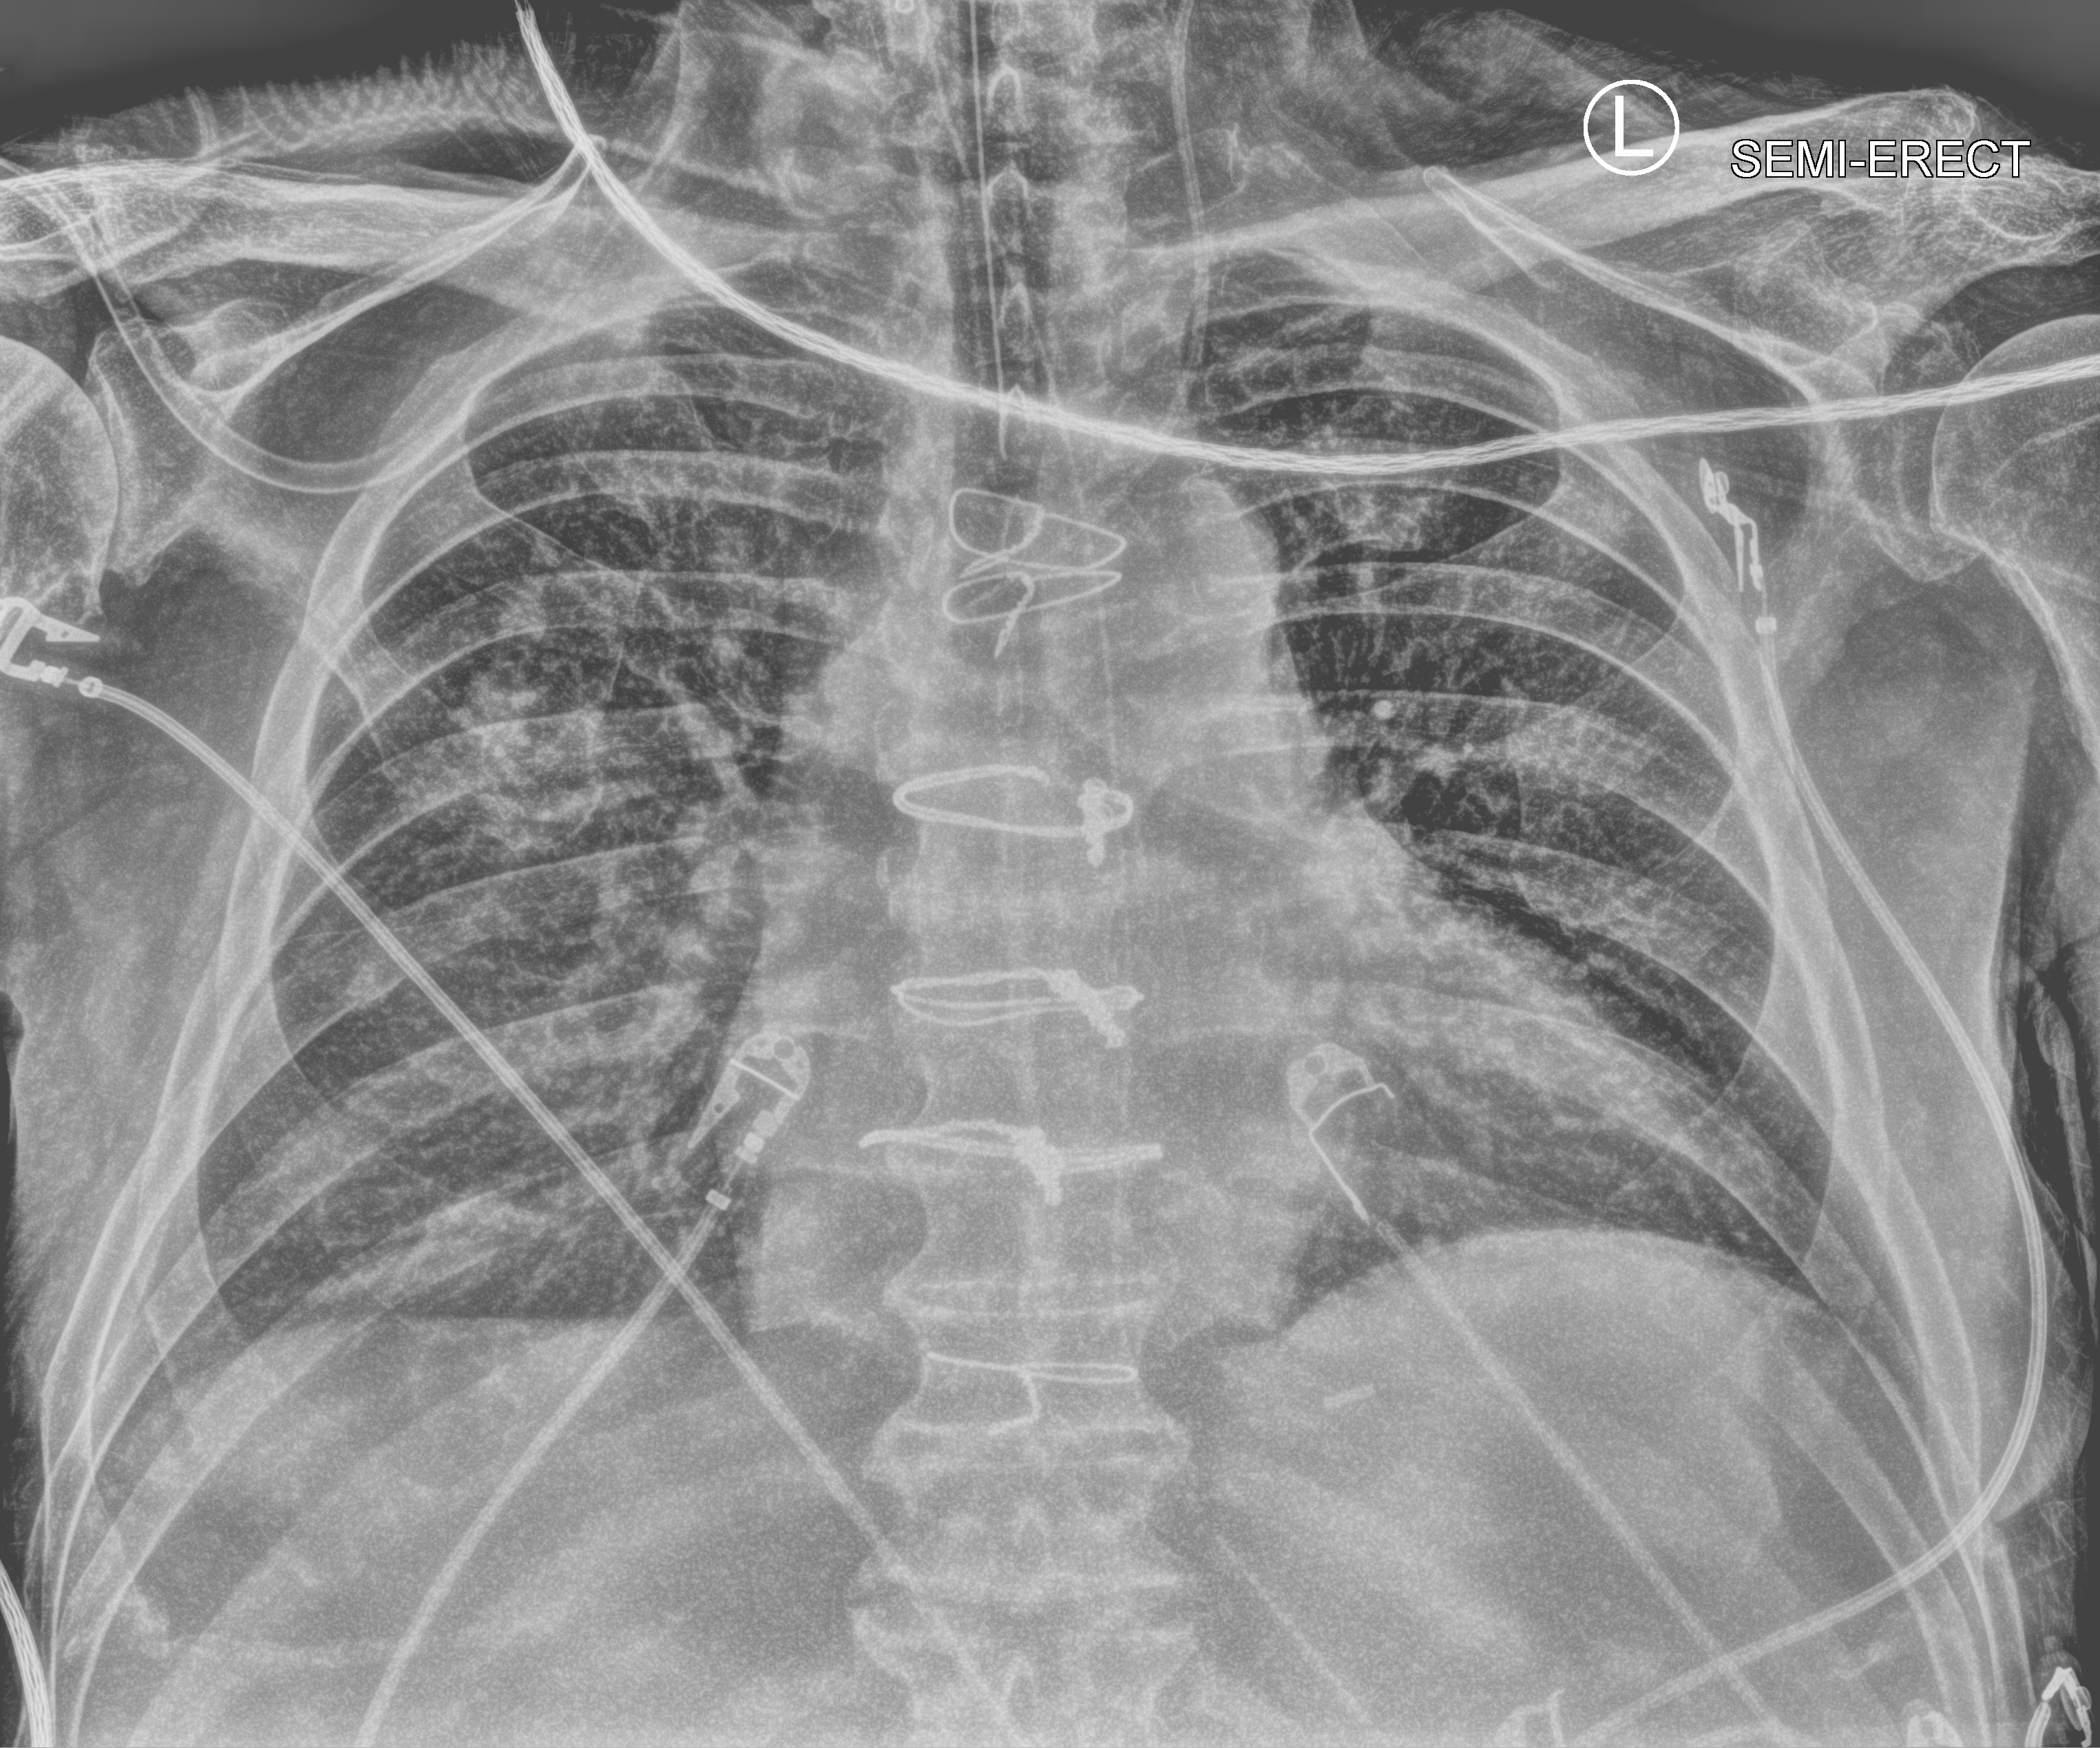
Chest X-ray (portable), anteroposterior (AP) projection. Patient hospitalised with COVID-19; male, aged 60–74 years.
From the hospital-stay record, not from the radiograph (when in the stay this image was taken is not recorded):
- mechanically ventilated during this hospital stay: yes
- admitted to intensive care during this hospital stay: yes
- length of hospital stay: 16 days